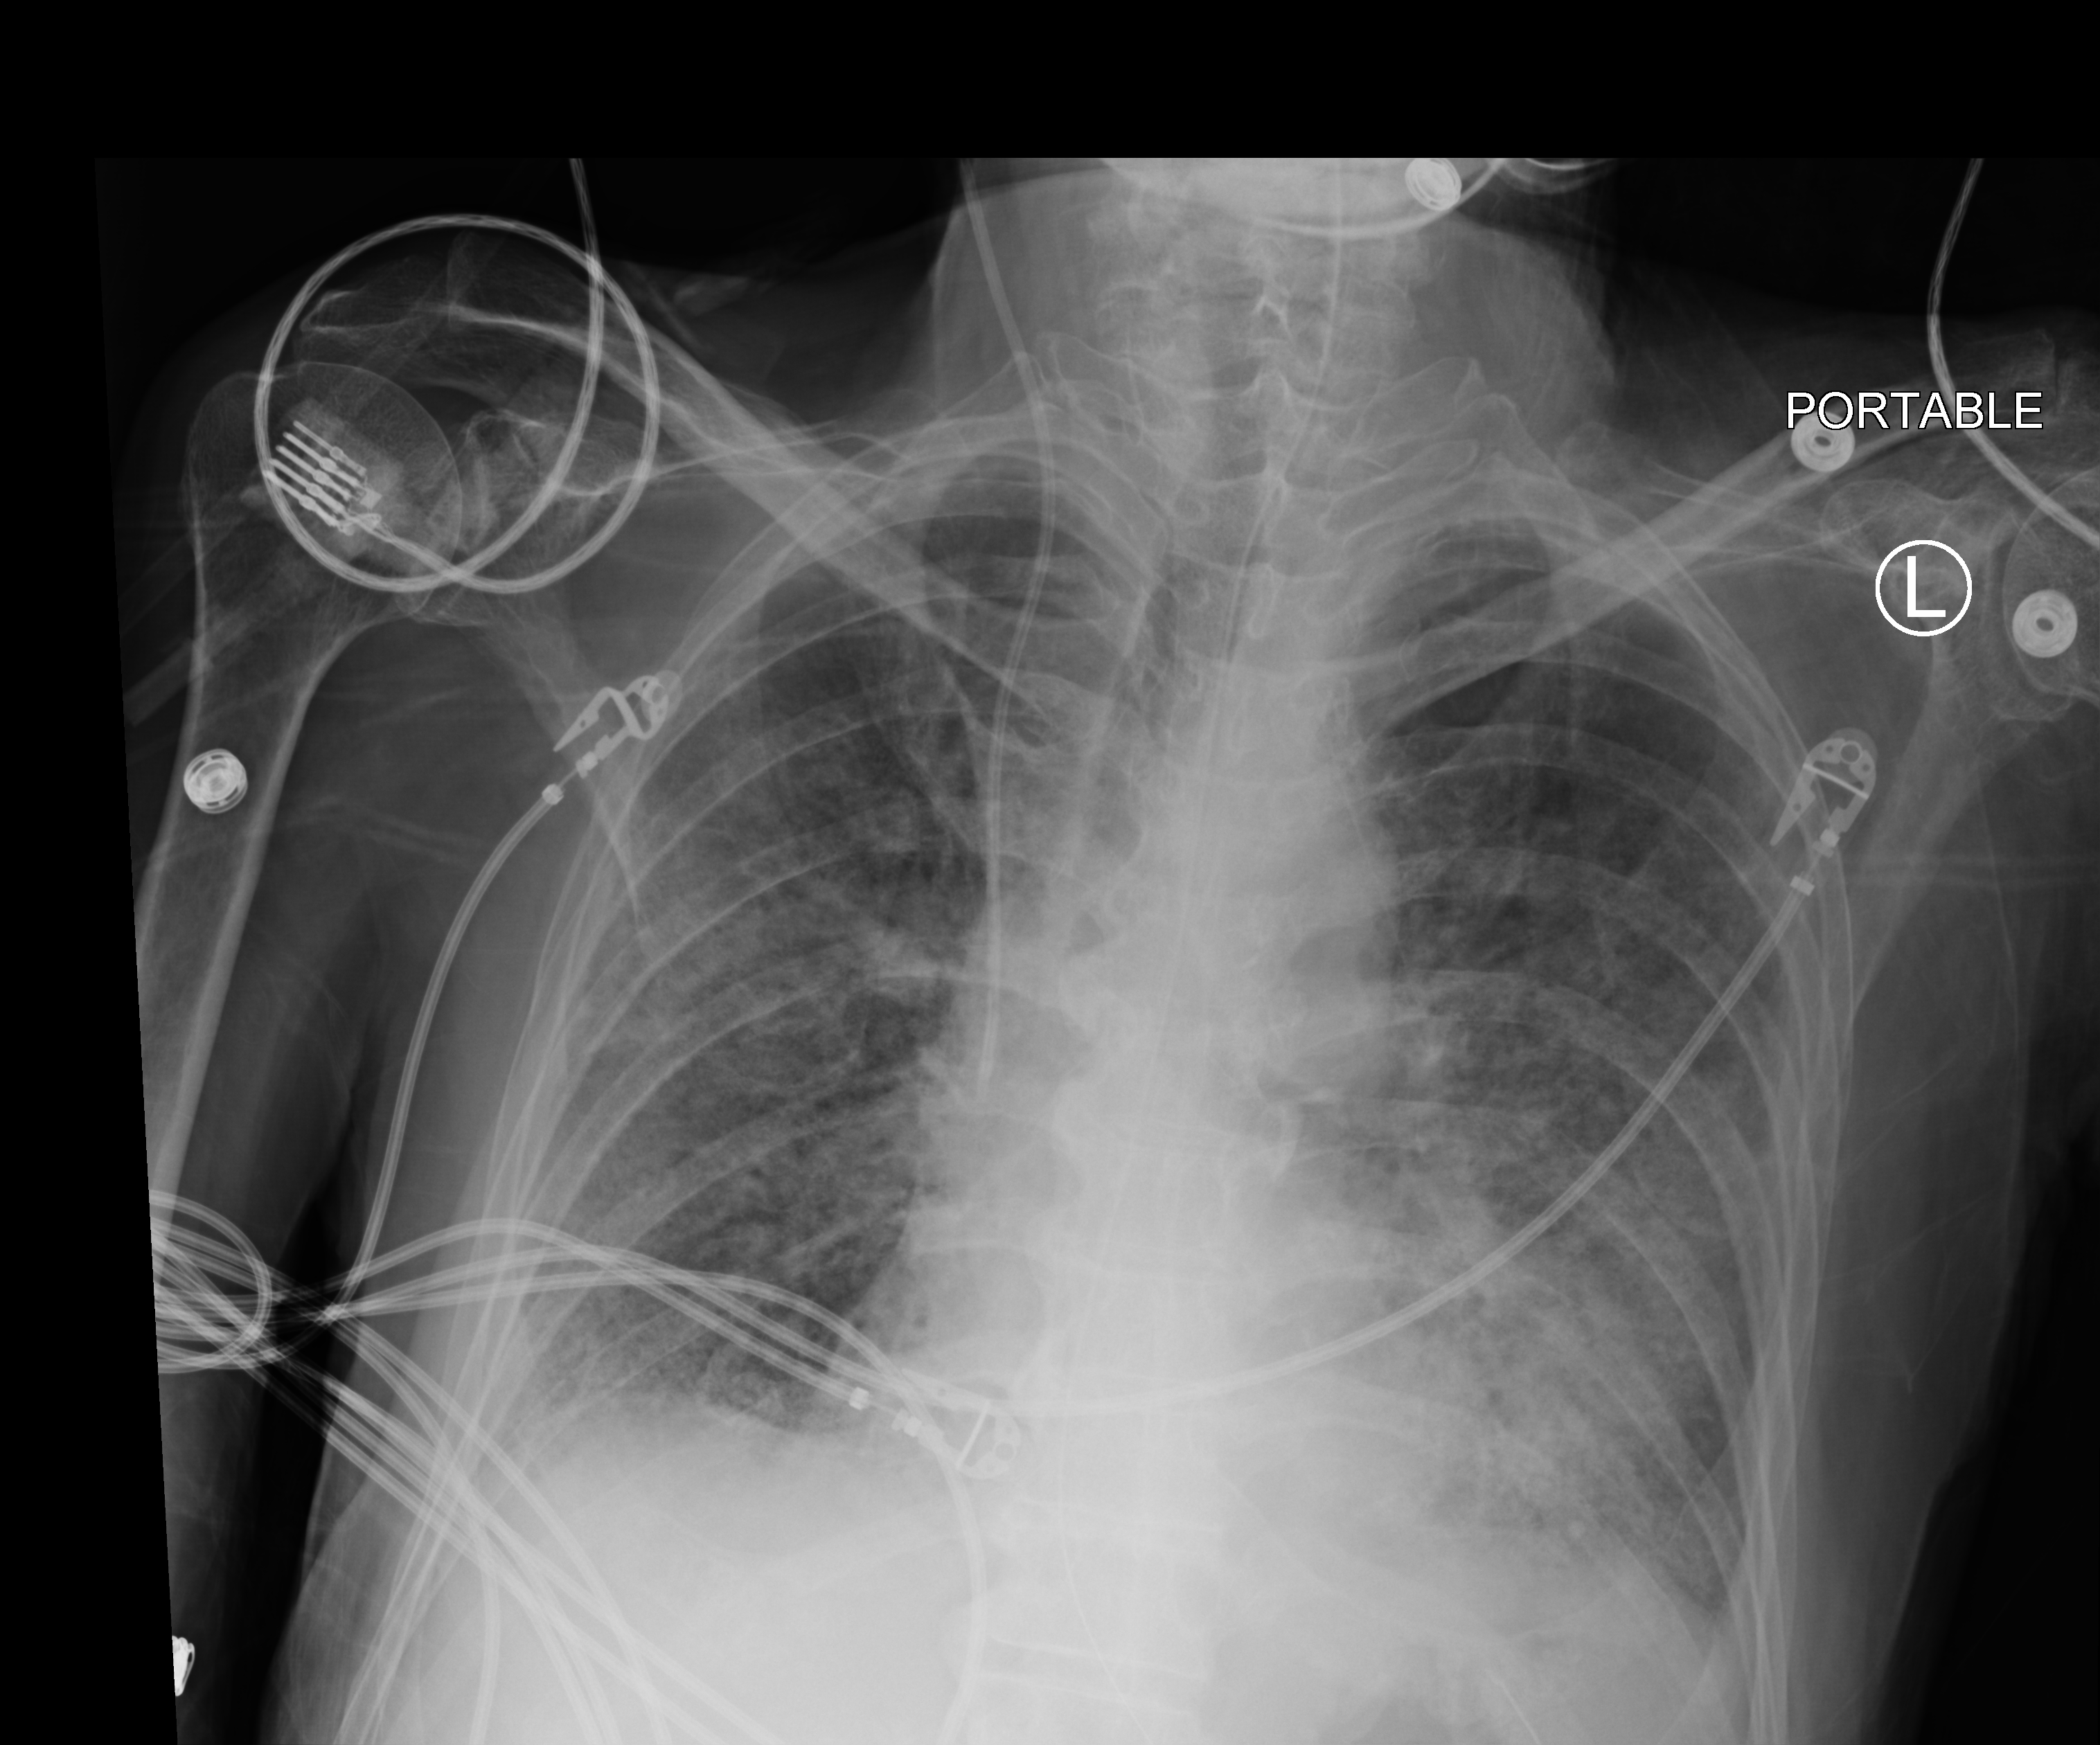
Portable chest radiograph. Male patient hospitalised with COVID-19, age 60–74 years.
Hospital-stay facts (about this admission, not read from this image; timing relative to this image not recorded):
- admitted to intensive care during this hospital stay: yes
- other chronic lung disease (admission record): no
- mechanically ventilated during this hospital stay: yes